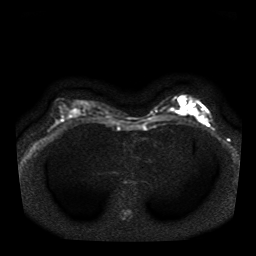
Breast MRI, one axial slice. Position 19 of 41 along the scan axis. Diffusion-weighted series; image 2 of 4 stored at this slice position (different b-values; order by instance number). 1.5 T. 256 × 256 image matrix, field of view 330 × 330 mm. Female patient.
Annotated regions visible in this slice (expert manual segmentation):
- tumour on diffusion-weighted imaging: bounding box [x1, y1, x2, y2] px = [190, 108, 197, 116]